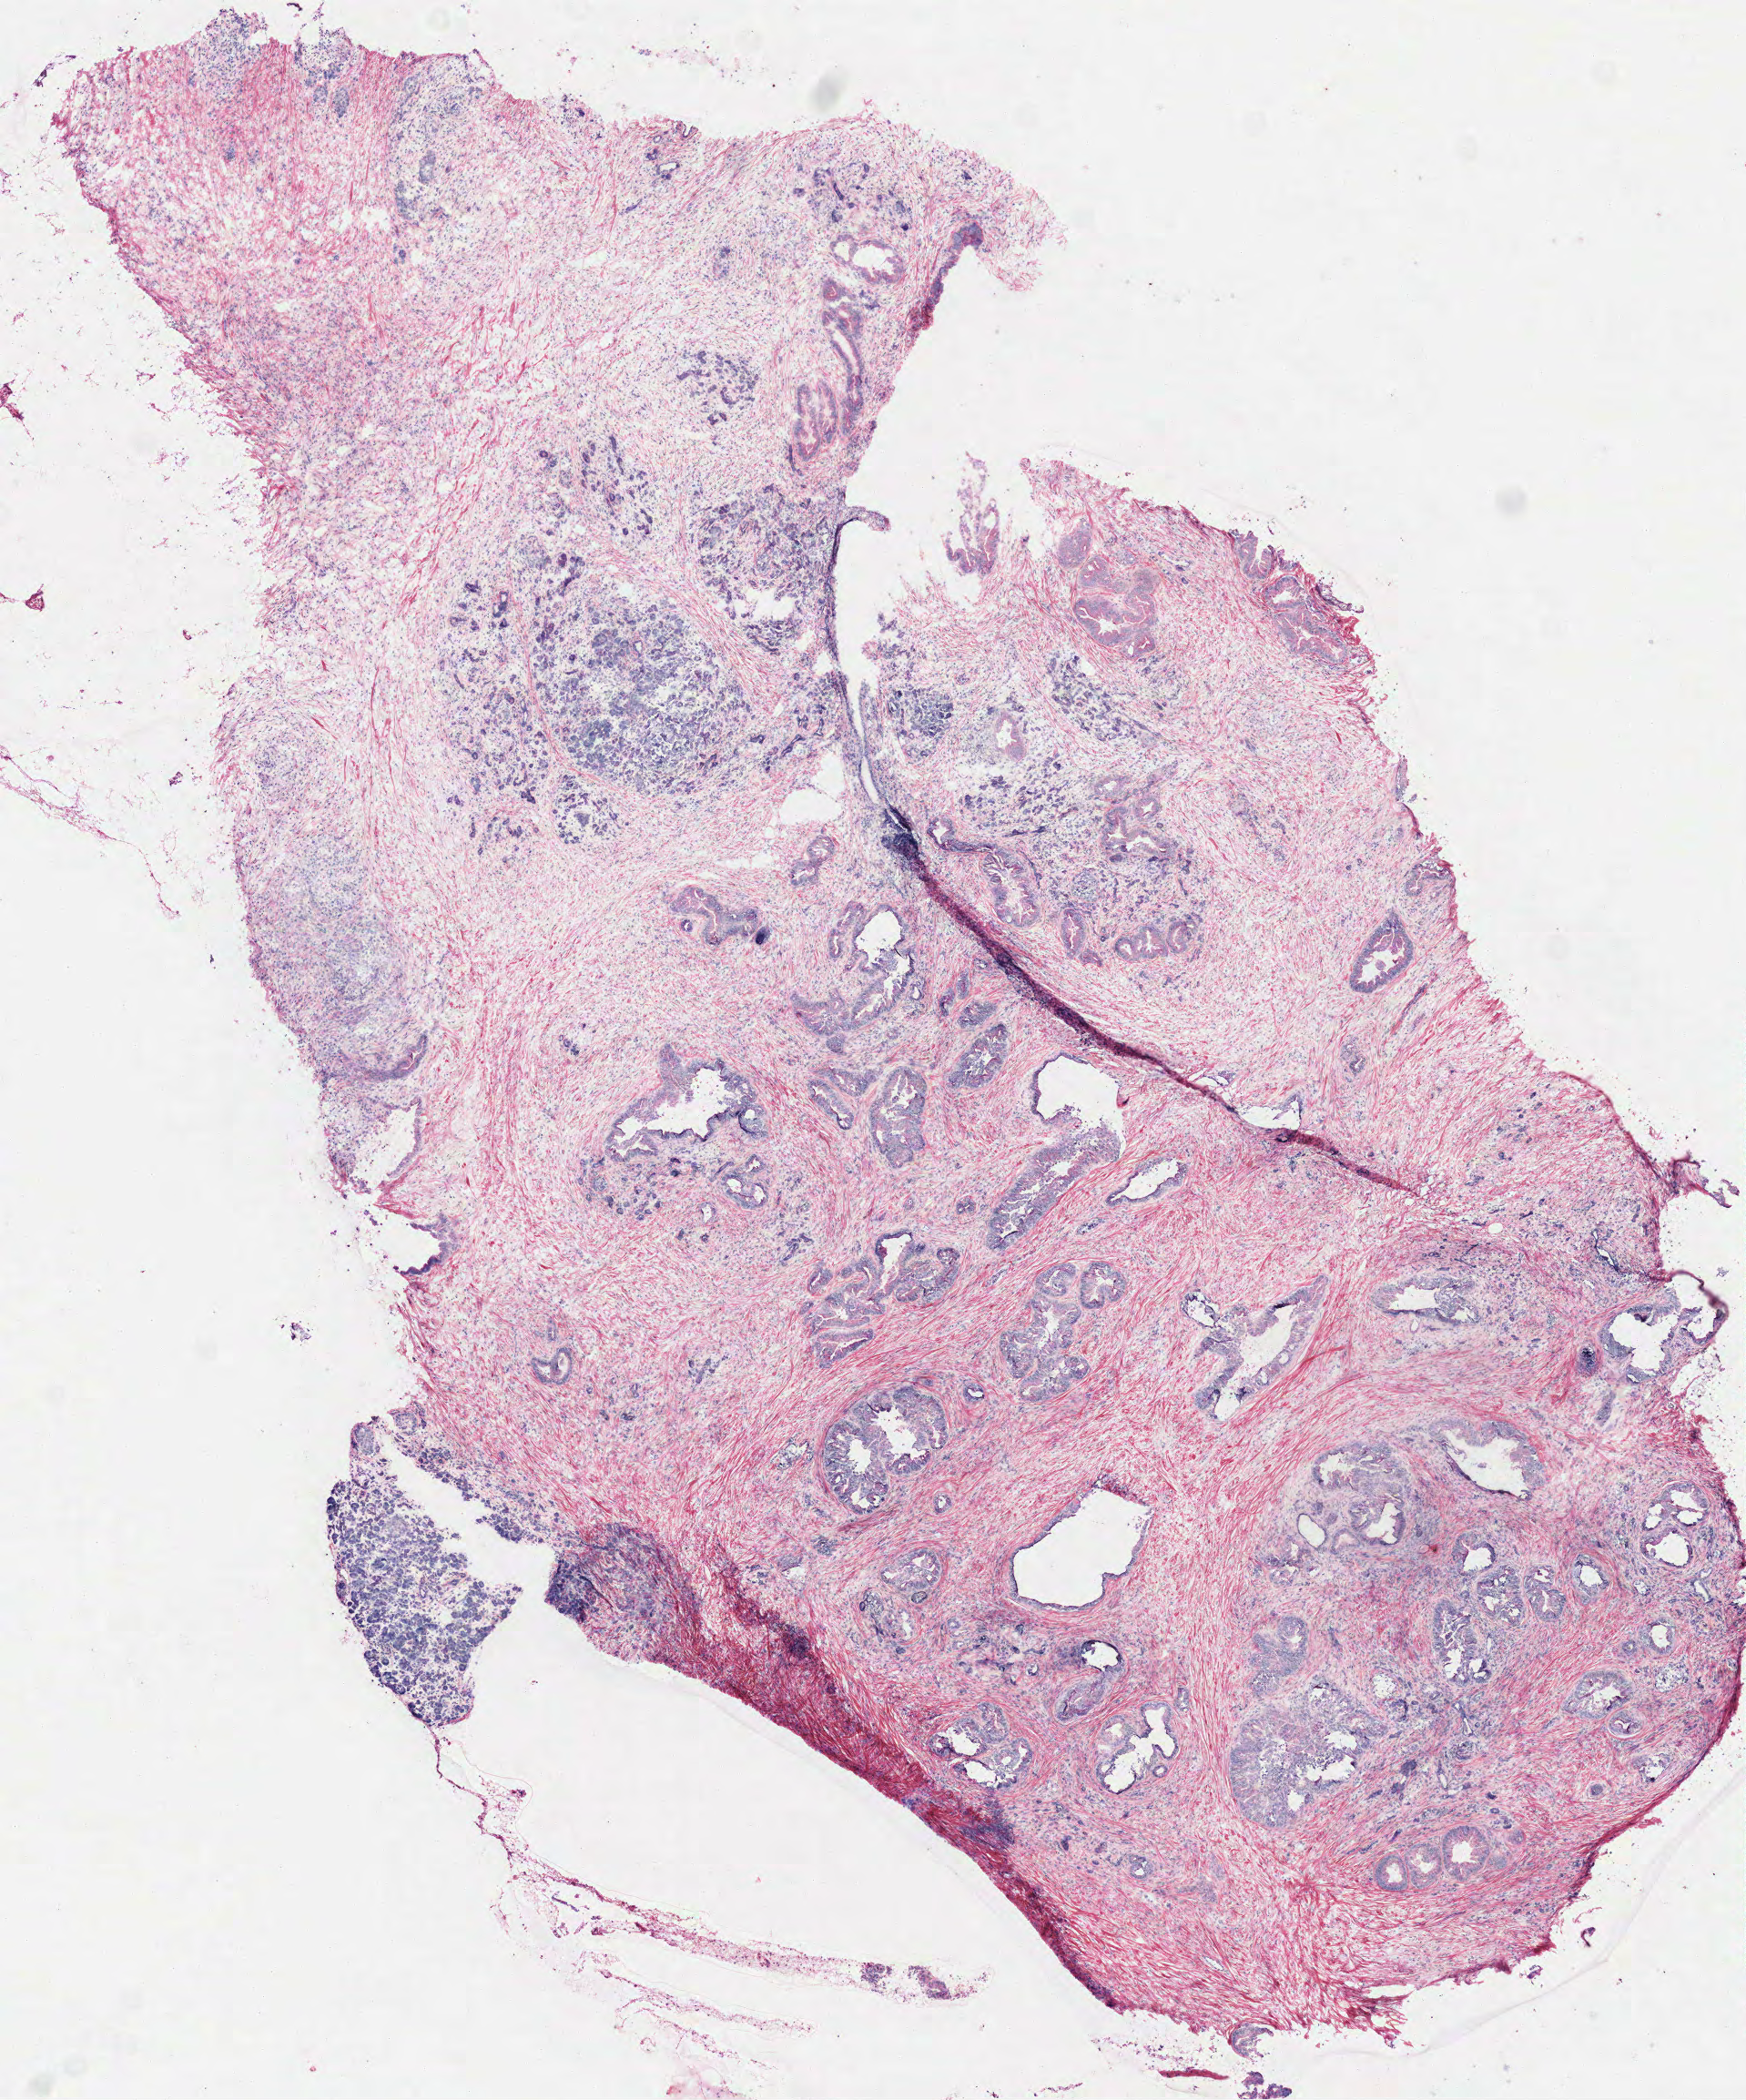
Digitized H&E tissue section (whole slide) — whole scanned area (about 7.7 x 9.3 mm) shown as a low-resolution overview; frozen section; sample: primary tumour, pancreas. Female patient; age at initial diagnosis 49 years. Histologic grade: G2 (moderately differentiated). Composition of this section per pathologist review: tumour cells 57%, tumour nuclei 60%, normal cells 4%, stromal cells 39%, necrosis 0%. Infiltration values recorded for this section: lymphocyte infiltration 5%, monocyte infiltration 0%, neutrophil infiltration 0%.
Pathologic diagnosis: Infiltrating duct carcinoma, NOS. AJCC pathologic stage: IIB. Lymph nodes positive (case pathology): 1 of 20 examined.